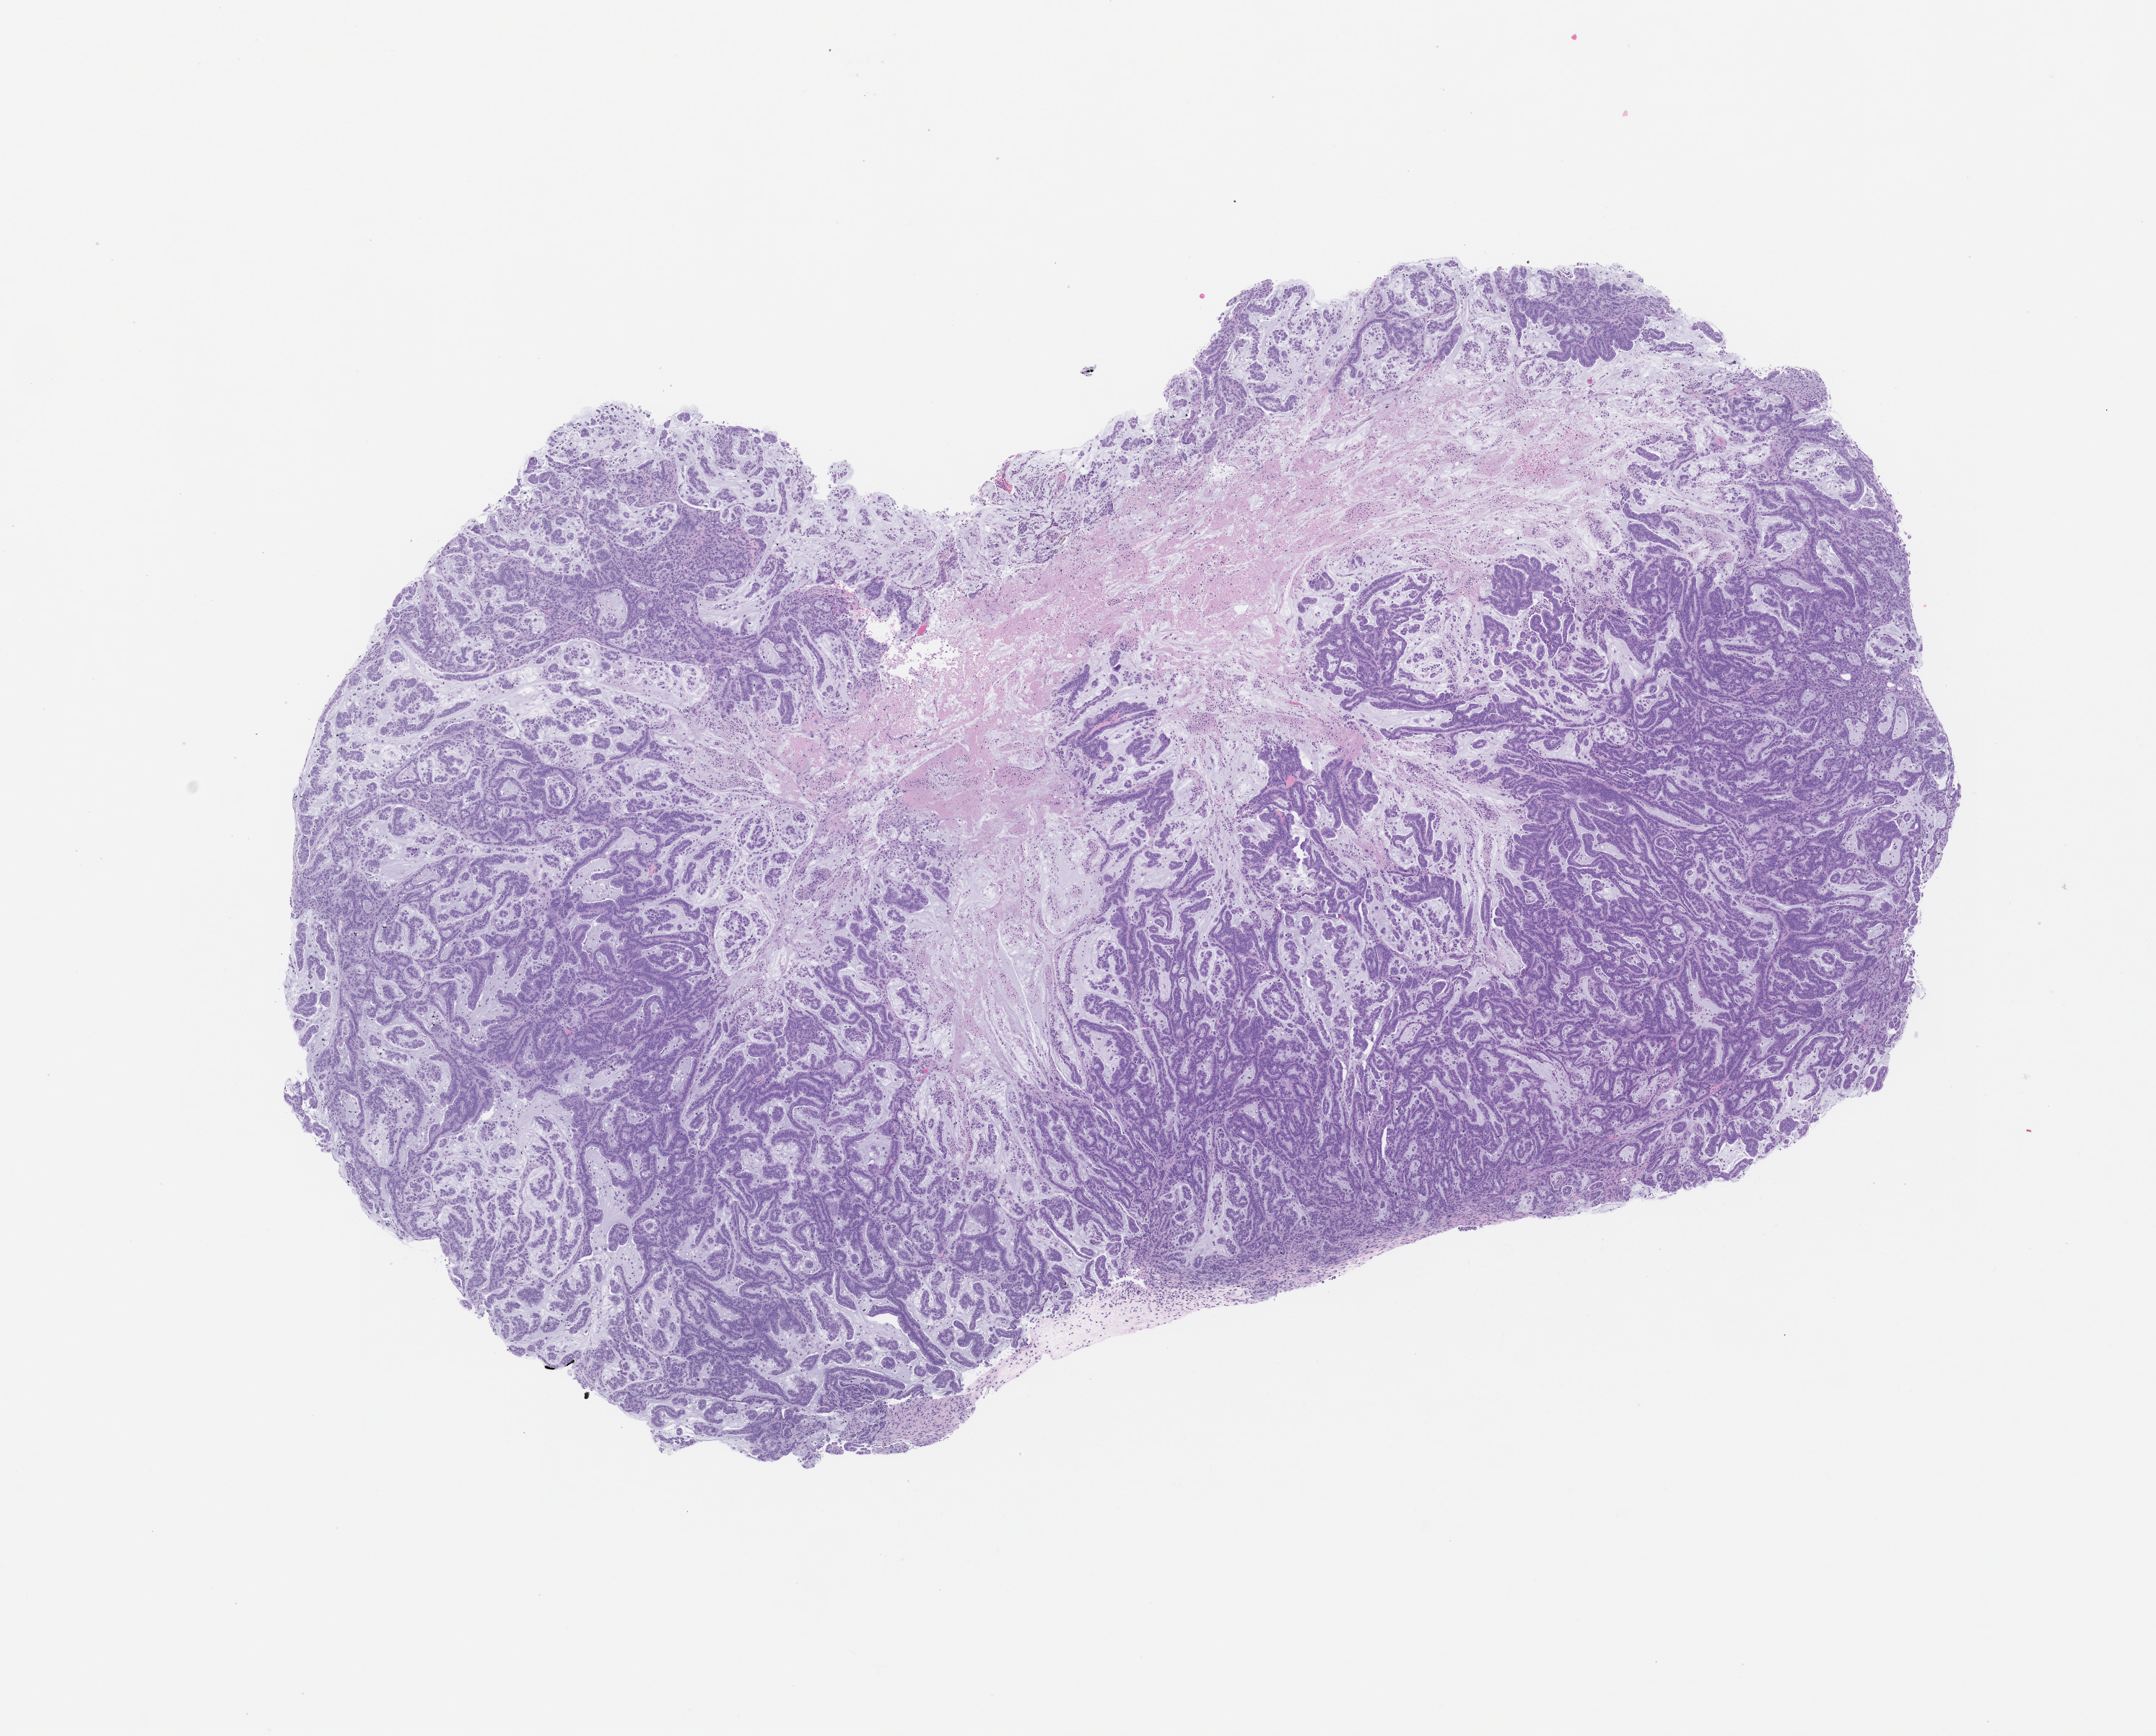
Haematoxylin and eosin whole-slide image of a patient-derived xenograft (PDX) tumor grown in a mouse, passage 1, low-resolution overview of the scanned area, about 12.0 x 9.6 mm; FFPE section; originating tumor site category: colon.
Originating patient diagnosis: Colon Adenocarcinoma.